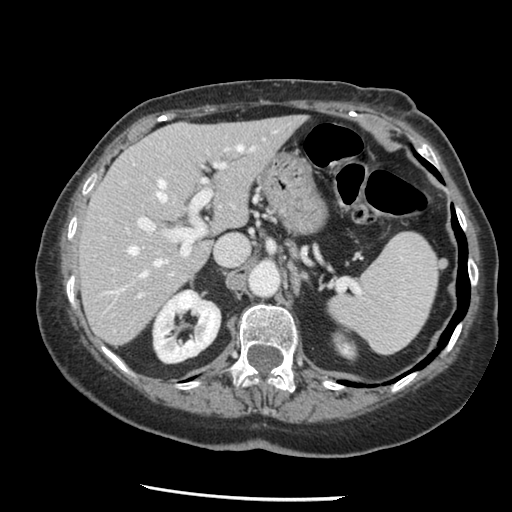
Contrast-enhanced abdominal CT, one axial slice; position 86 of 148 along the scan axis; reconstruction kernel STANDARD; soft-tissue window (W 400 / L 40 HU); 2.5 mm slice thickness; 512 × 512 image matrix, field of view 330 × 330 mm. Female patient, age 85 years. Case-level facts recorded for this patient, not image findings: diagnosis: colorectal cancer liver metastases, imaged before liver resection; multiple liver metastases: no; largest metastasis: 0.9 cm; disease in both lobes: no.
Annotated regions visible in this slice (manually delineated by an expert):
- hepatic veins: bounding box [x1, y1, x2, y2] px = [128, 147, 243, 278]
- liver: [81, 118, 301, 345]
- planned liver remnant (the part of the liver to remain after resection): [81, 118, 301, 345]
- portal vein (with intrahepatic branches): [139, 147, 230, 255]